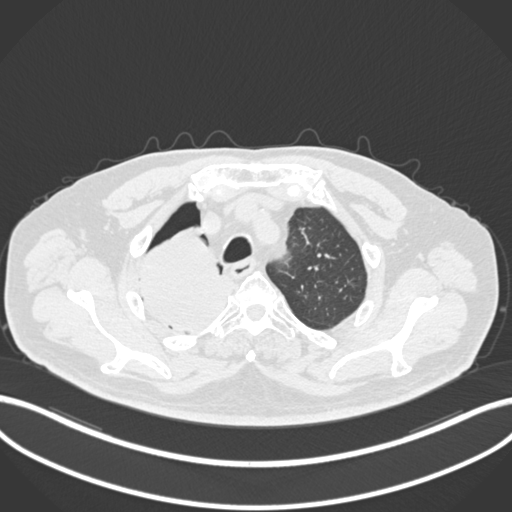
Chest CT, one axial slice; reconstruction kernel B30f; 120 kVp; lung window (W 1500 / L -600 HU); 512 × 512 image matrix, field of view 400 × 400 mm. Male patient, age 68 years. From the clinical record (not read from this slice): clinical TNM (as recorded): T2a N0 M0.
Structures marked on this image (rectangle marked by the reading radiologist):
- lung tumour (recorded histology: adenocarcinoma): bounding box <132,225,234,342> (left, top, right, bottom; pixels)